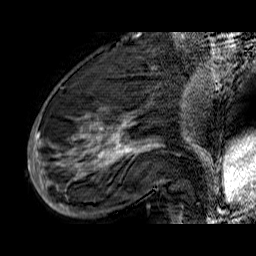
Breast MRI (dynamic contrast-enhanced), one sagittal slice; position 21 of 60 along the scan axis; dynamic contrast-enhanced series, time point 2 of 6 at this slice position (early post-contrast); 1.5 T; TE 6.5 ms, TR 32.9 ms; 4 mm slice thickness; 256 × 256 image matrix, field of view 200 × 200 mm. Female patient. Case-level facts recorded for this patient, not image findings: setting: breast cancer imaged before/during neoadjuvant chemotherapy; receptor status: HR-positive, HER2-negative.
Annotated regions visible in this slice (semi-automatic segmentation, software-assisted and operator-edited):
- analysis volume of interest (the breast-tissue region the enhancement analysis was run in; not a lesion): bounding box <33,74,176,210> (left, top, right, bottom; pixels)
- tumour enhancement mask (voxels above the 100 % enhancement threshold inside the analysis volume of interest): <33,109,148,210>